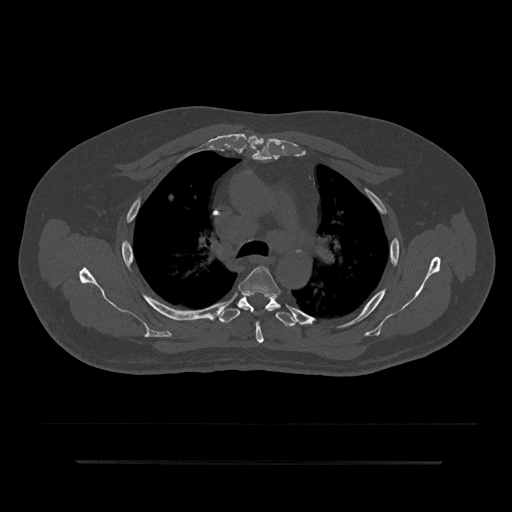
CT including the spine, one axial slice; position 598 of 797 along the scan axis; 120 kVp; bone window (W 1800 / L 400 HU); 0.5 mm slice thickness; 512 × 512 image matrix, field of view 464 × 464 mm. Male patient, age 59 years. From the clinical record (not read from this slice): primary cancer: bile ducts; vertebrae with lytic lesions (as recorded): T10.
Annotated regions visible in this slice (semi-automatically segmented with operator editing):
- T4 vertebra: box from (x=239, y=266) to (x=281, y=344) px
- T5 vertebra: (x=219, y=293)–(x=297, y=327)